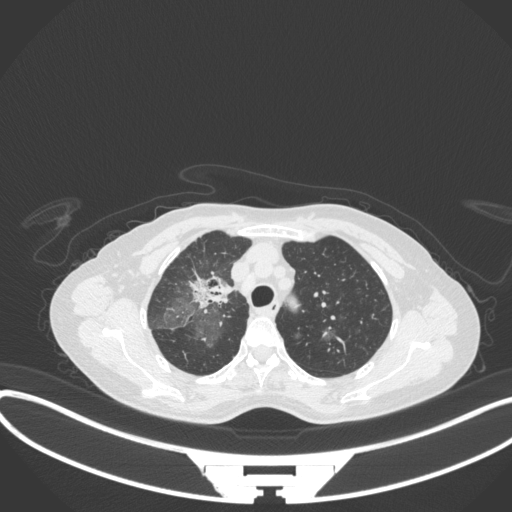
Chest CT, one axial slice. Lung window (W 1500 / L -600 HU). 1 mm slice thickness. 512 × 512 image matrix, field of view 400 × 400 mm. Female patient, age 59 years. Case-level facts recorded for this patient, not image findings: clinical TNM (as recorded): T3 N0 M0.
Structures marked on this image (rectangle marked by the reading radiologist):
- lung tumour (recorded histology: adenocarcinoma): box from (x=185, y=269) to (x=230, y=320) px